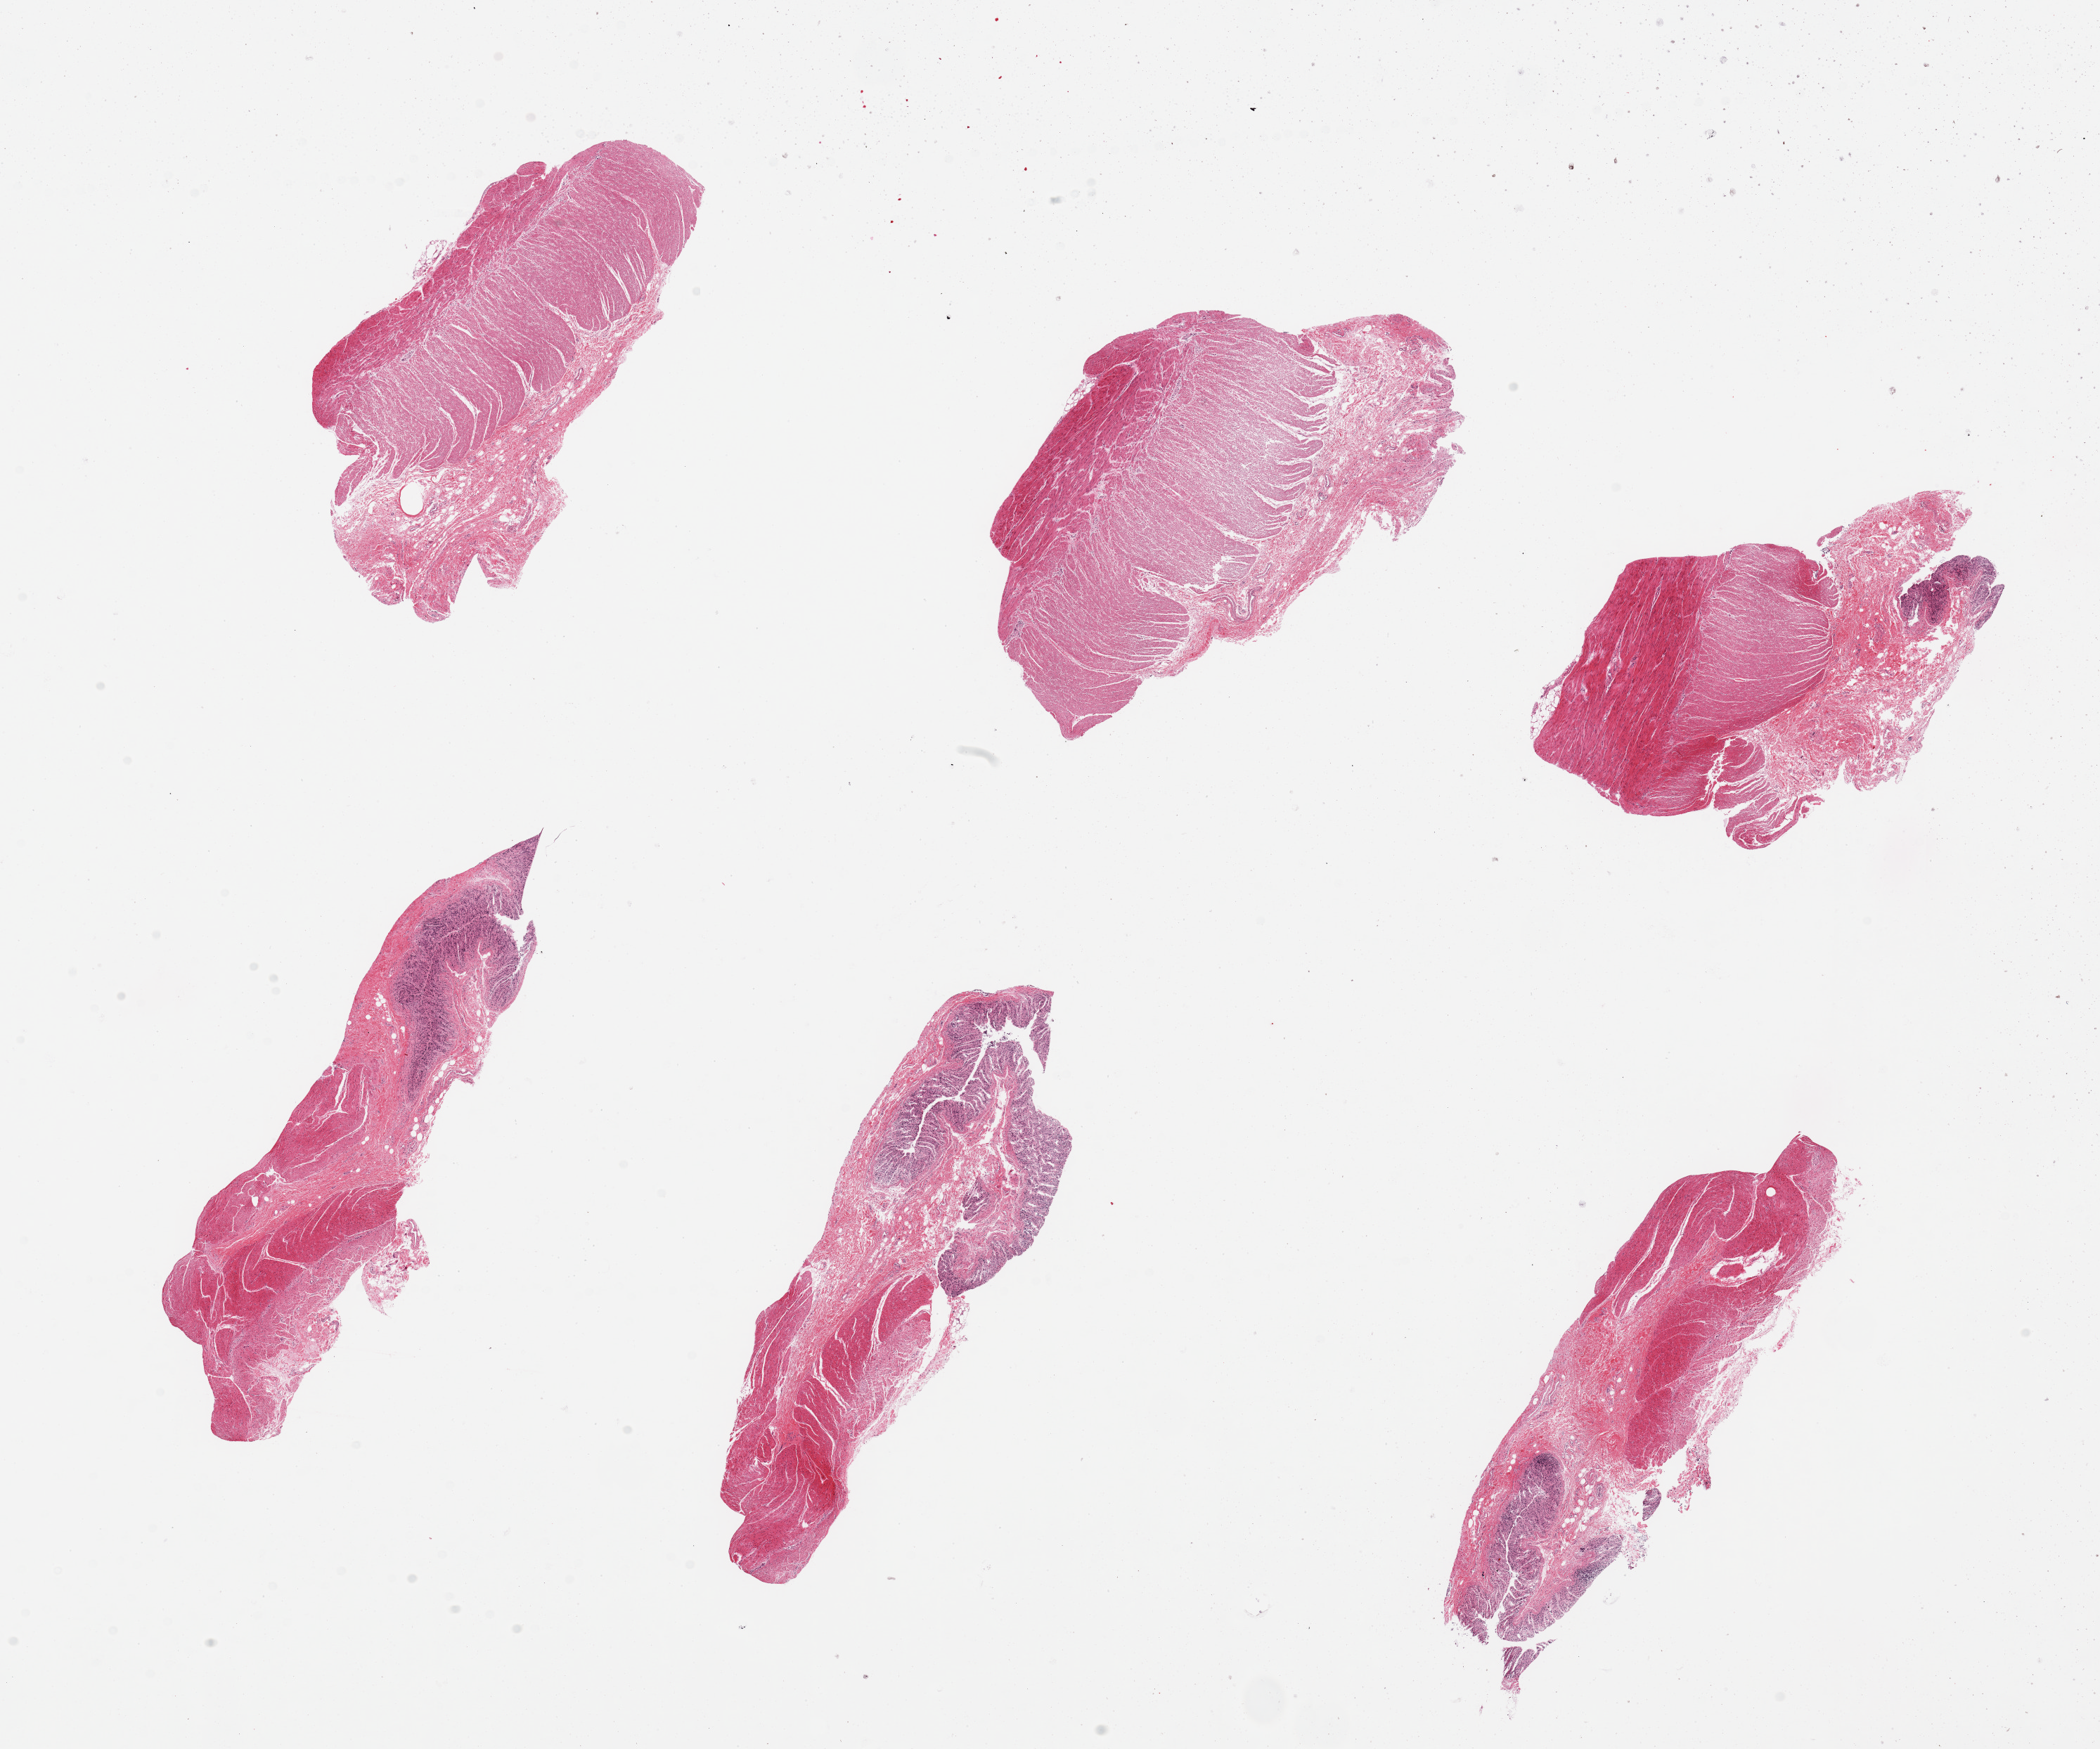
Whole-slide image, hematoxylin and eosin (H&E) stain — whole scanned area (about 23.6 x 19.7 mm, slide scanned at 20x) shown as a low-resolution overview; PAXgene-fixed, paraffin-embedded tissue; target tissue: sigmoid colon; tissue donor sample.
• reviewer comment on this tissue sample: 6 pieces. Muscle (target) is moderately autolyzed; mucosa (not target) is severly autolyzed, 4 of 6 contain mucosa